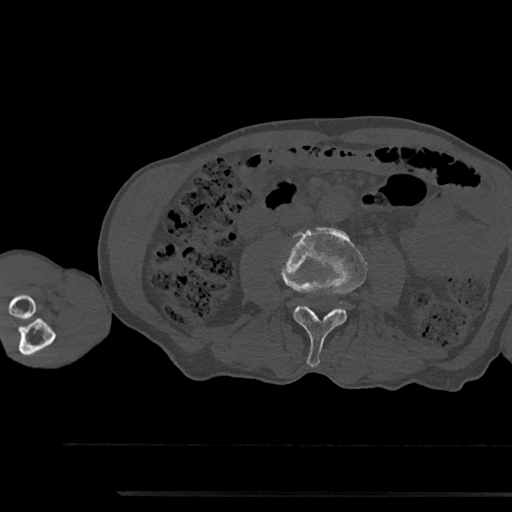
CT including the spine, one axial slice; slice 468 of 797 in the series (ordered by position); 120 kVp; bone window (W 1800 / L 400 HU); 0.5 mm slice thickness; 512 × 512 image matrix, field of view 367 × 367 mm. Male patient, age 79 years. Case-level facts recorded for this patient, not image findings: primary cancer: prostate.
Outlined on this slice (semi-automatically segmented with operator editing):
- L3 vertebra: bounding box <281,227,367,367> (left, top, right, bottom; pixels)